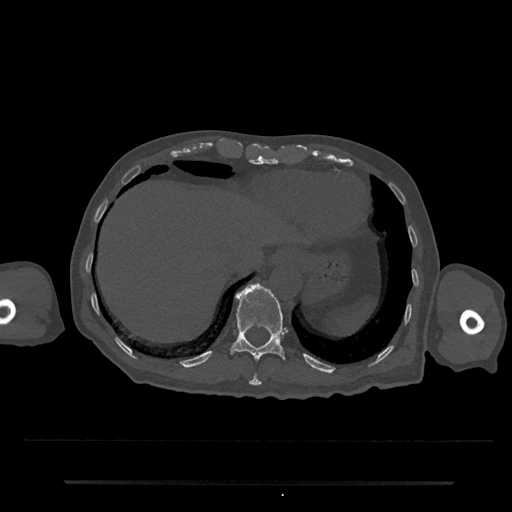
CT including the spine, one axial slice; slice 258 of 797 in the series (ordered by position); 120 kVp; bone window (W 1800 / L 400 HU); 0.5 mm slice thickness; 512 × 512 image matrix, field of view 427 × 427 mm. Male patient, age 74 years. From the clinical record (not read from this slice): primary cancer: prostate.
Structures marked on this image (semi-automatic segmentation, software-assisted and operator-edited):
- T10 vertebra: bounding box (x1, y1, x2, y2) in pixels: (249, 373, 262, 386)
- T11 vertebra: (230, 283, 288, 362)